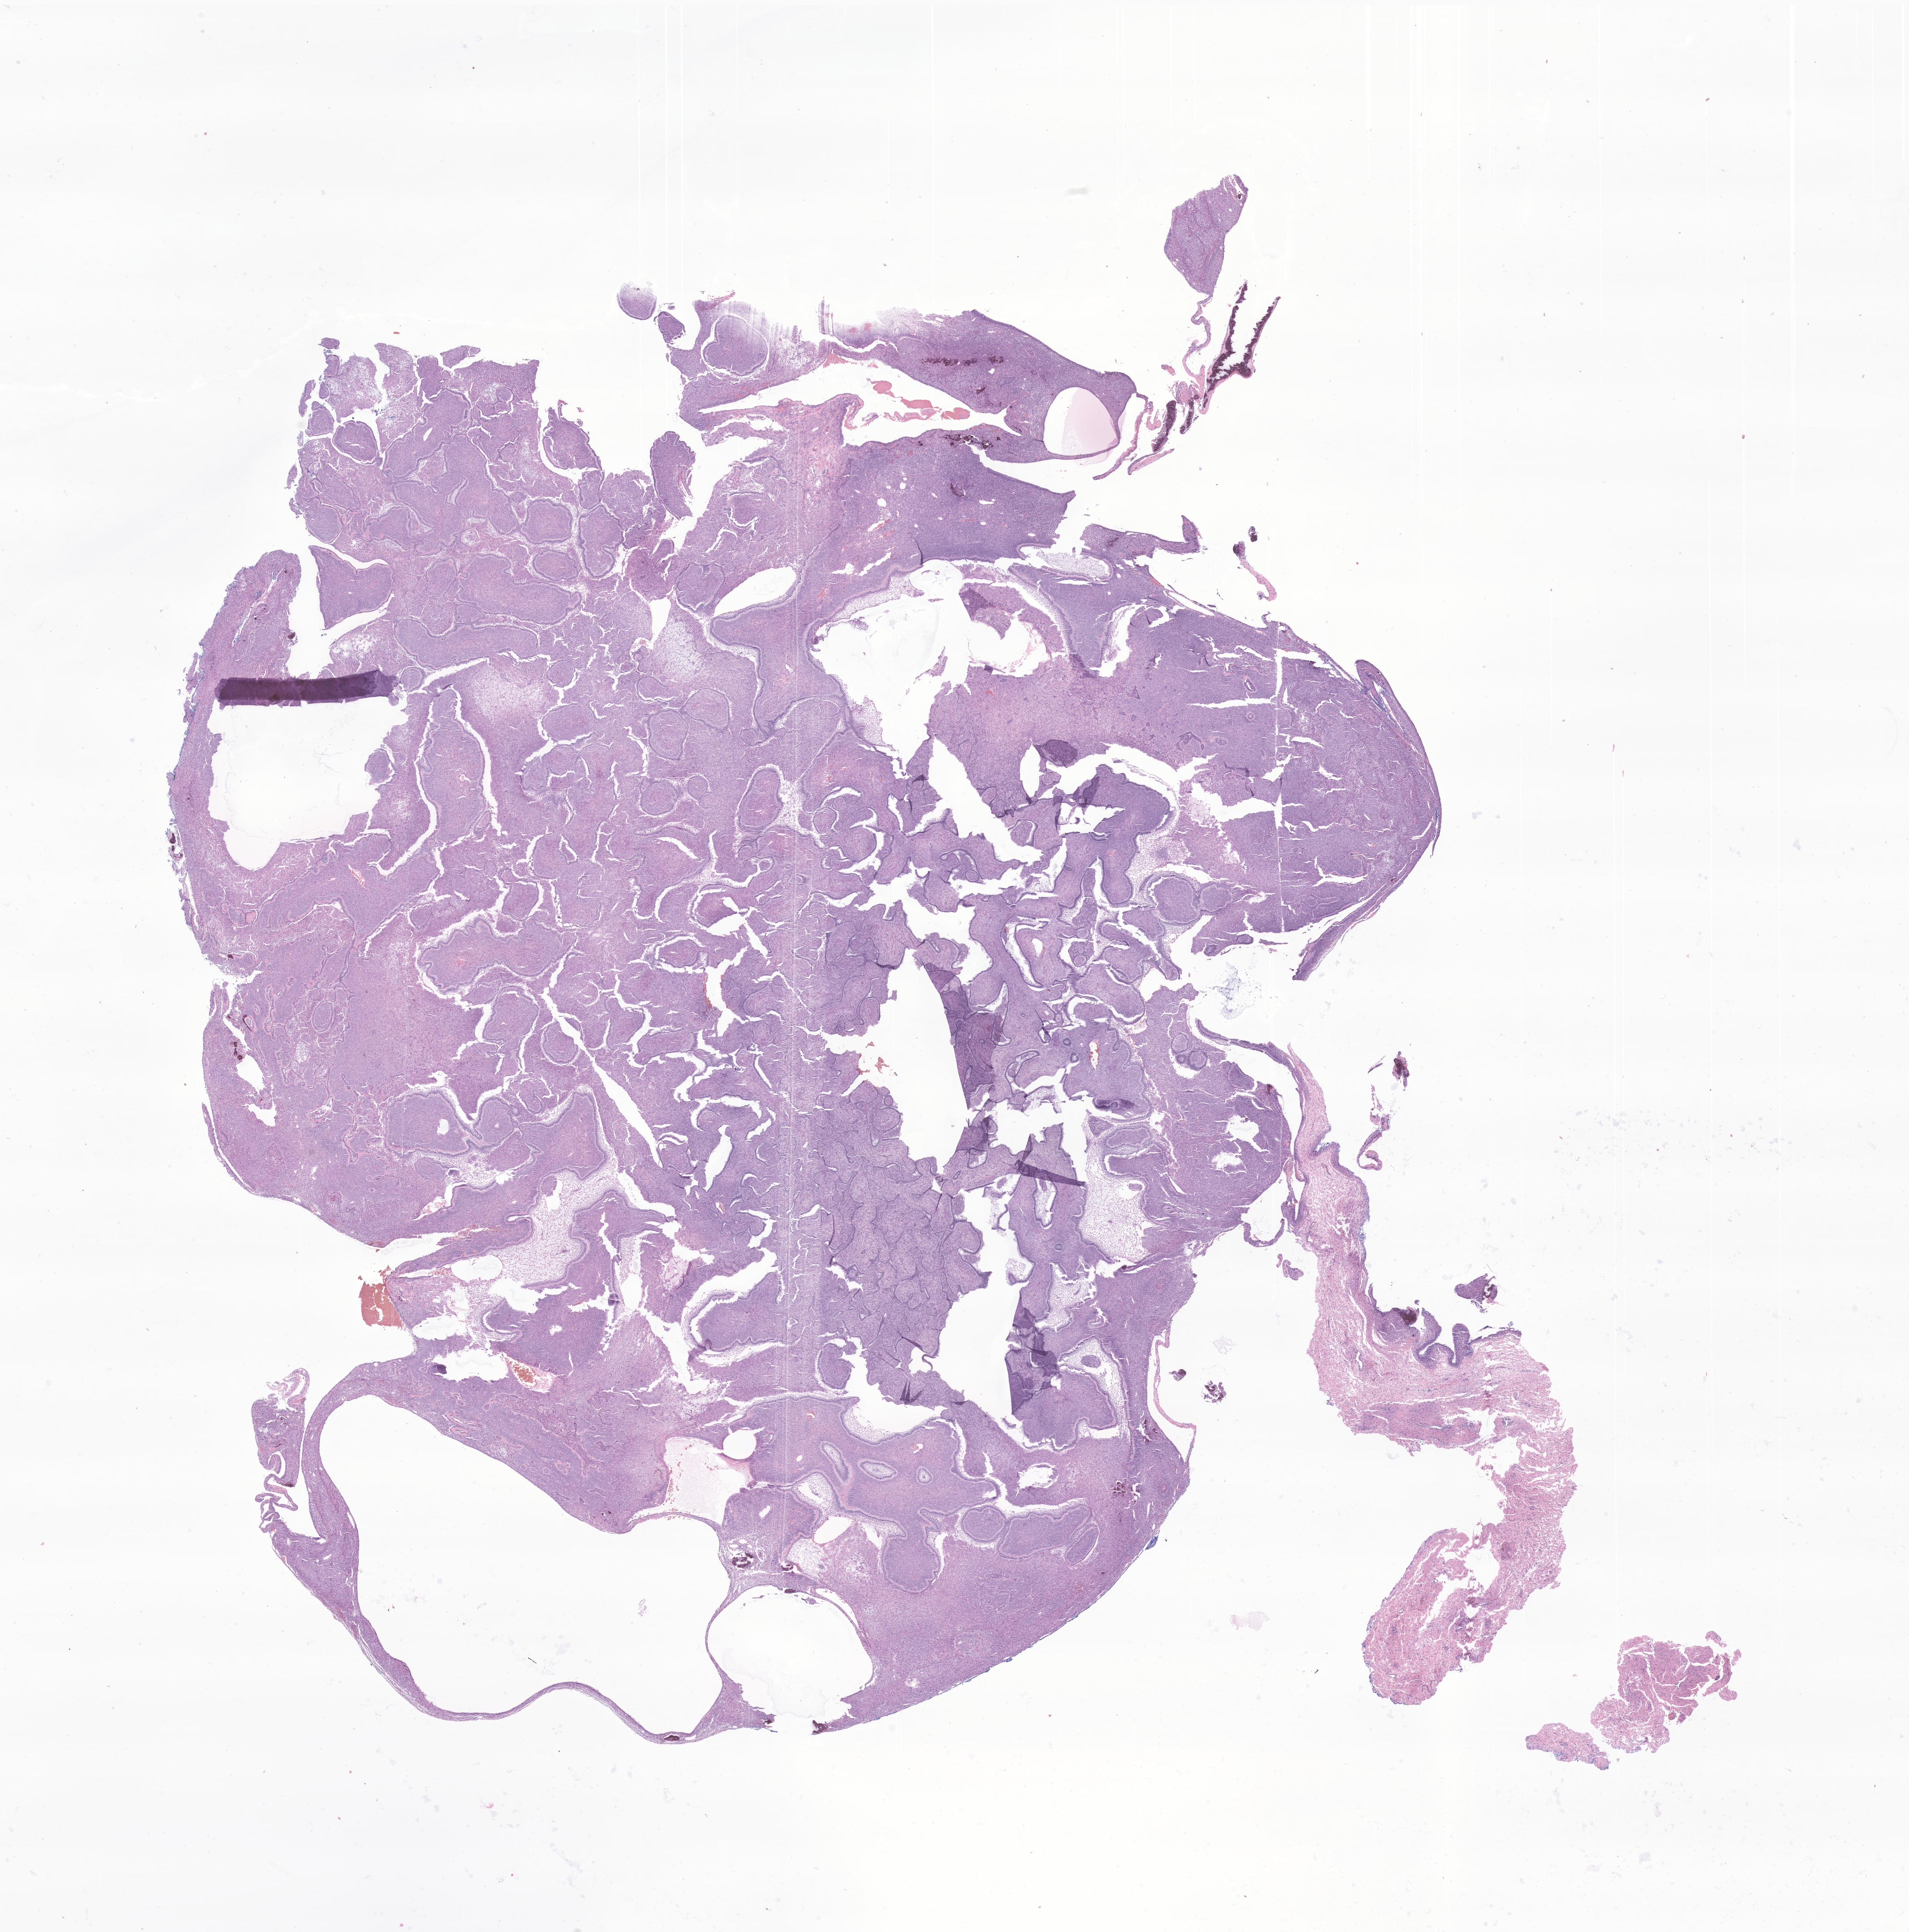
Hematoxylin and eosin (H&E) whole-slide image of tumor tissue from the maxillary sinus — shown as a low-resolution overview of the whole scanned area (about 20.9 x 21.2 mm), formalin-fixed paraffin-embedded section. Male patient, age 131 months (10 years 11 months).
* diagnosis (ICD-O-3 morphology term): Odontogenic carcinosarcoma